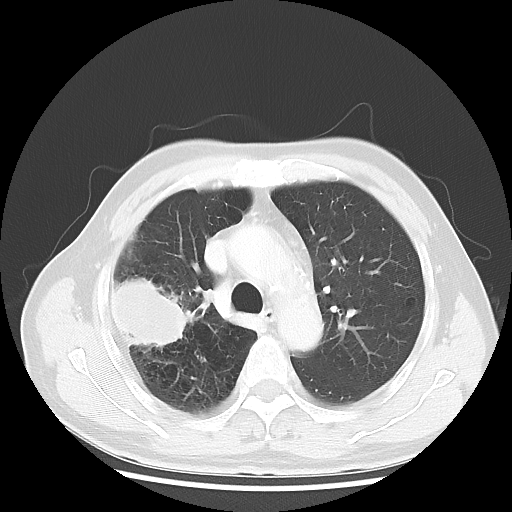
Chest CT, one axial slice. Slice 35 of 50 in the series (ordered by position). Reconstruction kernel LUNG. 120 kVp. Lung window (W 1500 / L -600 HU). 512 × 512 image matrix, field of view 360 × 360 mm. Male patient, age 69 years. From the clinical record (not read from this slice): clinical TNM (as recorded): T3 N0 M0; histopathological grade: G3.
Structures marked on this image (bounding box drawn by a radiologist):
- lung tumour (recorded histology: adenocarcinoma): box from (x=112, y=275) to (x=193, y=351) px